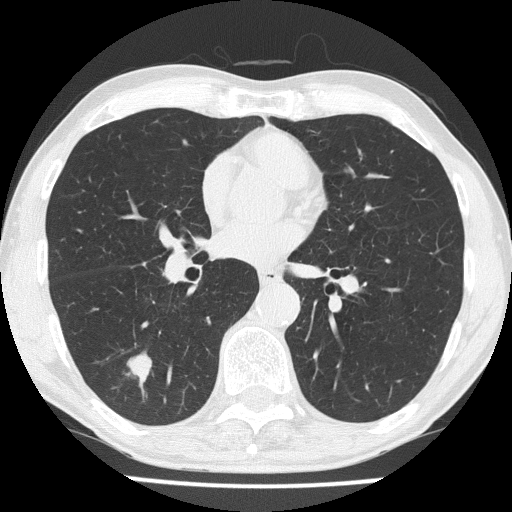
Low-dose screening chest CT, one axial slice; slice 81 of 186 in the series (ordered by position); reconstruction kernel FC51; 120 kVp; lung window (W 1500 / L -600 HU); 512 × 512 image matrix, field of view 328 × 328 mm.
Outlined on this slice (manually delineated by an expert):
- lesion 1 (tumor, lower lobe of right lung): bounding box [x1, y1, x2, y2] px = [127, 351, 152, 384]